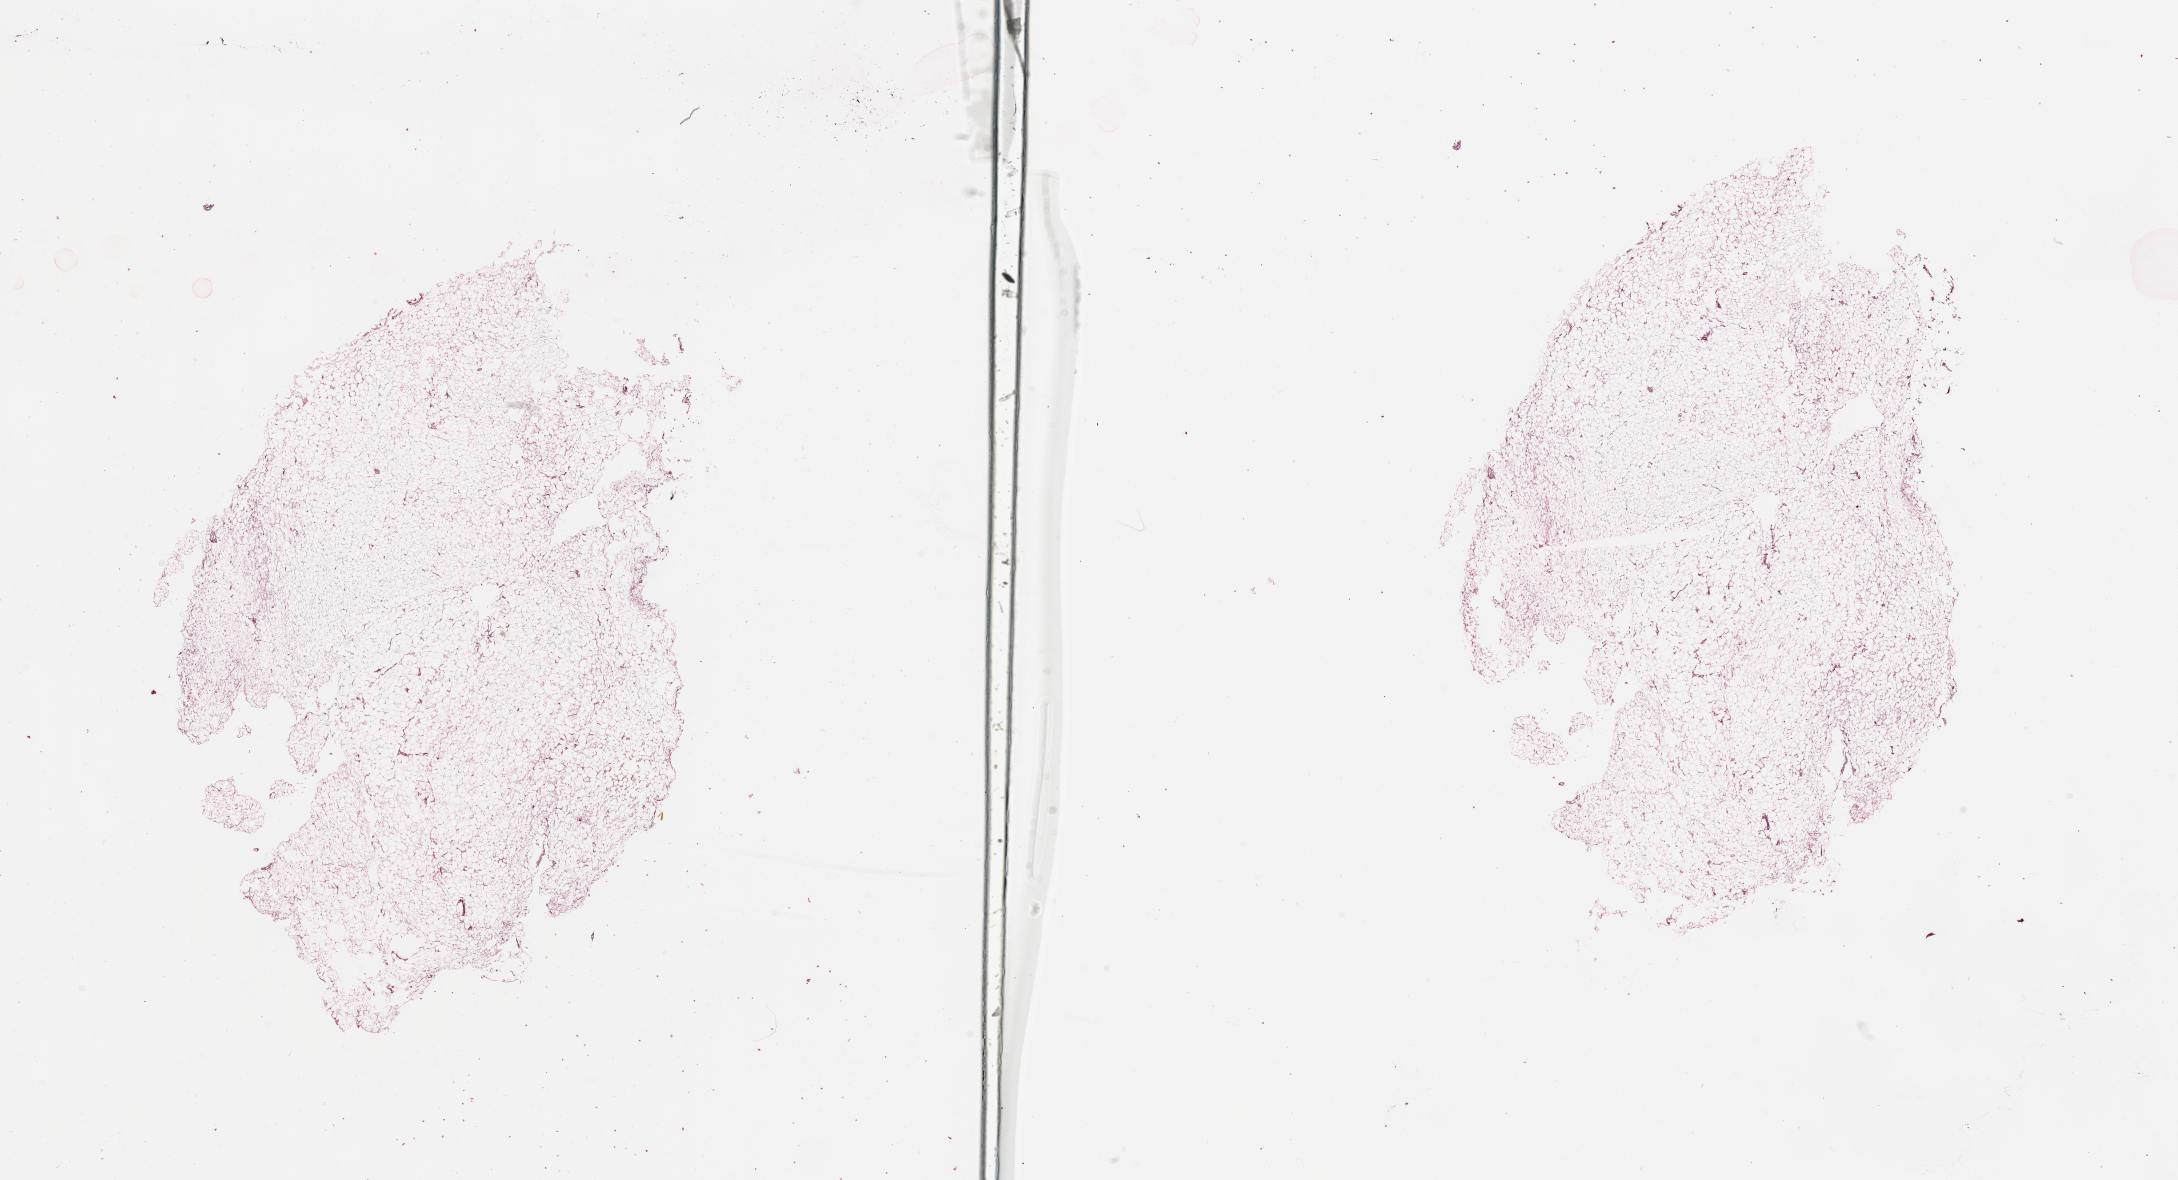
H&E-stained whole-slide image, shown as a low-resolution overview of the whole scanned area (about 34.5 x 18.7 mm), kidney, normal (non-tumour) tissue. Male, 58 y/o.
This section: normal (non-tumour) tissue from the same patient. Patient diagnosis: Renal cell carcinoma, NOS.